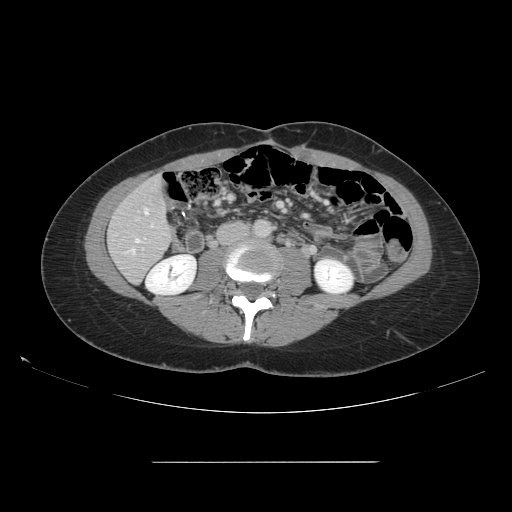
Contrast-enhanced abdominal CT, one axial slice; intravenous contrast given; soft-tissue window (W 400 / L 40 HU); 512 × 512 image matrix. Female patient, age 46 years. Case-level facts recorded for this patient, not image findings: diagnosis: colorectal cancer liver metastases, imaged before liver resection; multiple liver metastases: yes; largest metastasis: 3 cm; disease in both lobes: yes.
Annotated regions visible in this slice (expert manual segmentation):
- hepatic veins: bounding box <133,208,149,253> (left, top, right, bottom; pixels)
- liver: <110,177,173,282>
- planned liver remnant (the part of the liver to remain after resection): <109,177,173,282>